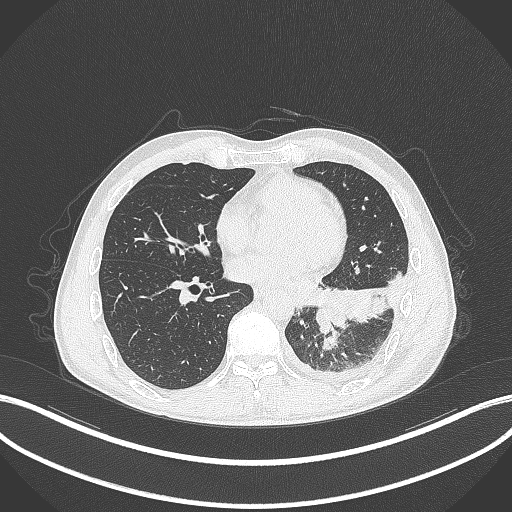
Chest CT, one axial slice. Slice 127 of 295 in the series (ordered by position). Reconstruction kernel B70f. Lung window (W 1500 / L -600 HU). 1 mm slice thickness. 512 × 512 image matrix, field of view 400 × 400 mm. Patient: male, 47 years. Case-level facts recorded for this patient, not image findings: clinical TNM (as recorded): T3 N1 M1c; histopathological grade: G3.
Outlined on this slice (bounding box drawn by a radiologist):
- lung tumour (recorded histology: small cell carcinoma): bounding box [x1, y1, x2, y2] px = [308, 285, 351, 333]